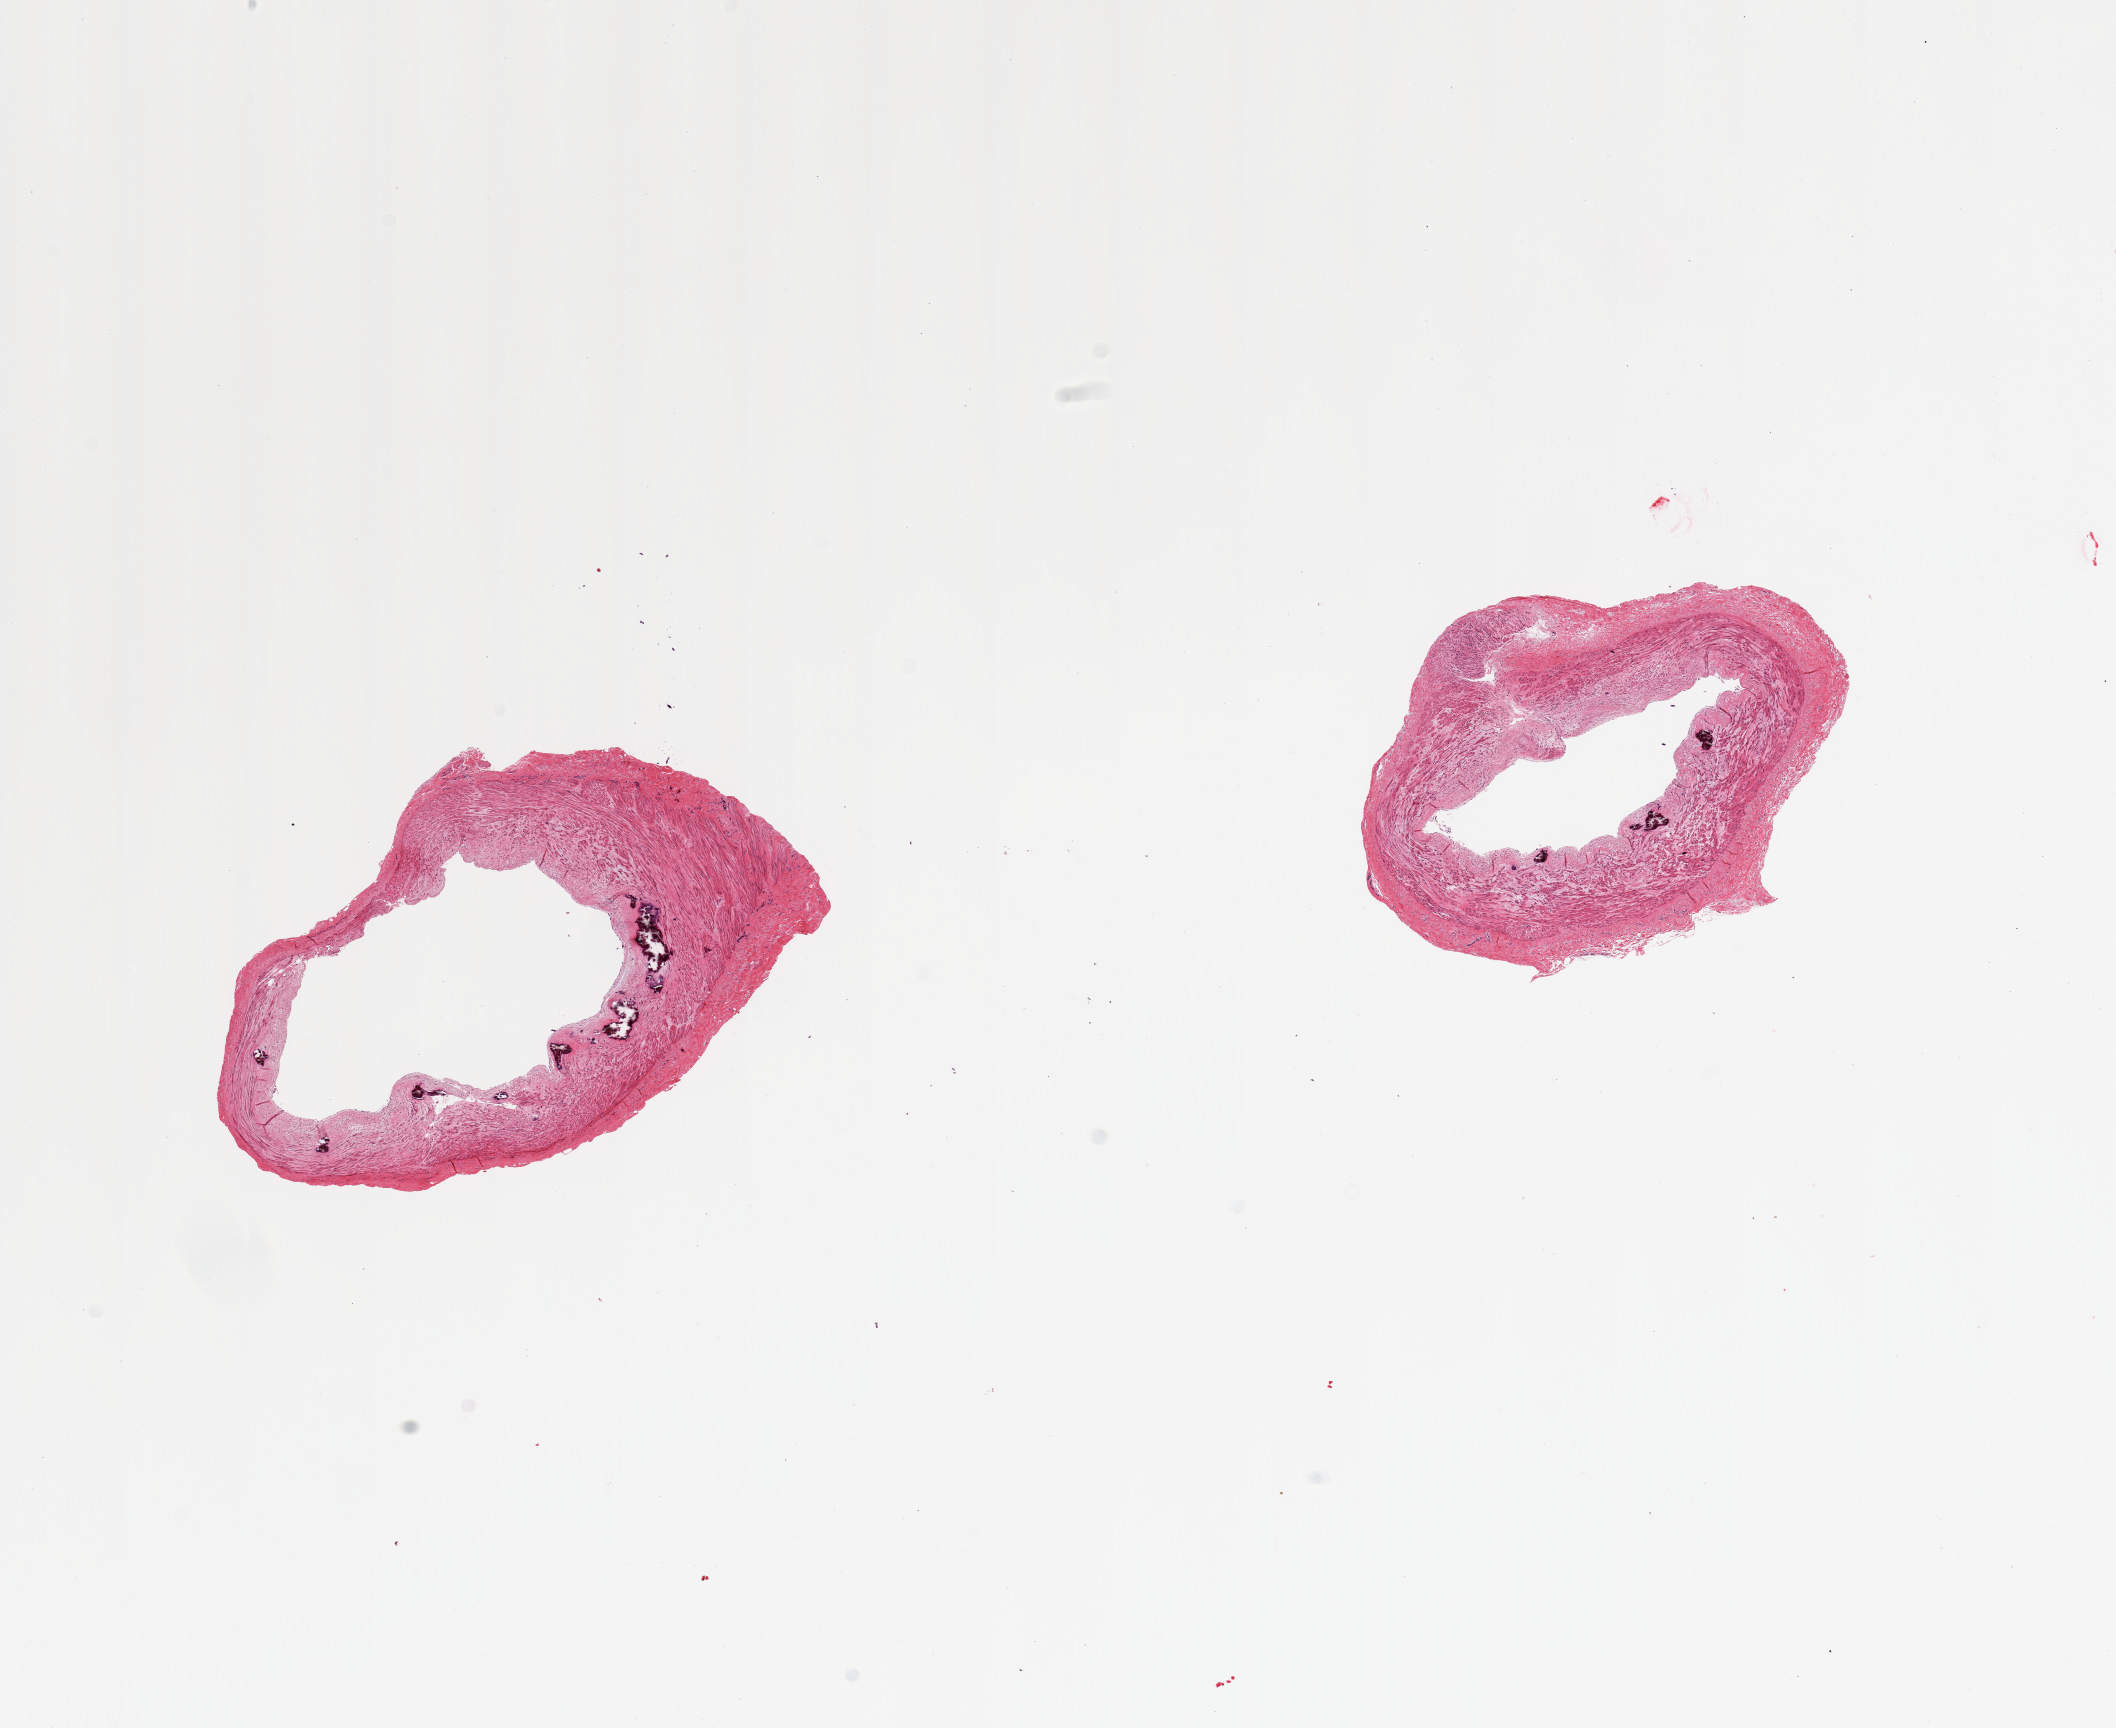
Digitized hematoxylin and eosin (H&E)-stained section — shown as a low-resolution overview of the whole scanned area (about 16.7 x 13.7 mm, slide scanned at 20x), PAXgene-fixed paraffin-embedded (PFPE) section, section of tibial artery (target tissue), donor tissue sample. Donor sex: female.
Review note (as recorded): 2 pieces; calcific atherosclerosis and medial calcification.